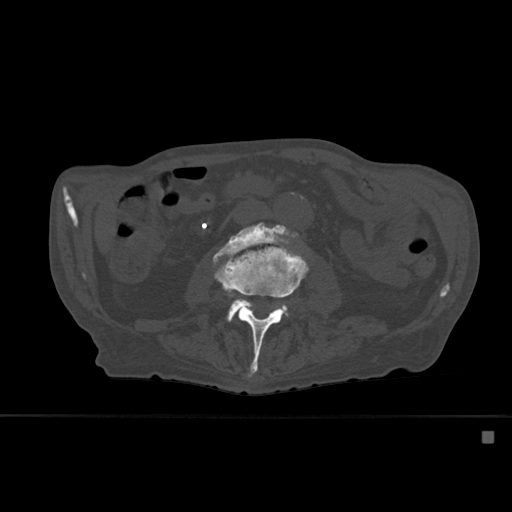
CT including the spine, one axial slice. Position 210 of 527 along the scan axis. Bone window (W 1800 / L 400 HU). 1.5 mm slice thickness. 512 × 512 image matrix, field of view 373 × 373 mm. Male patient, age 78 years. Case-level facts recorded for this patient, not image findings: primary cancer: prostate.
Structures marked on this image (semi-automatically segmented with operator editing):
- L3 vertebra: bounding box (x1, y1, x2, y2) in pixels: (213, 230, 309, 376)
- L4 vertebra: (214, 227, 291, 321)